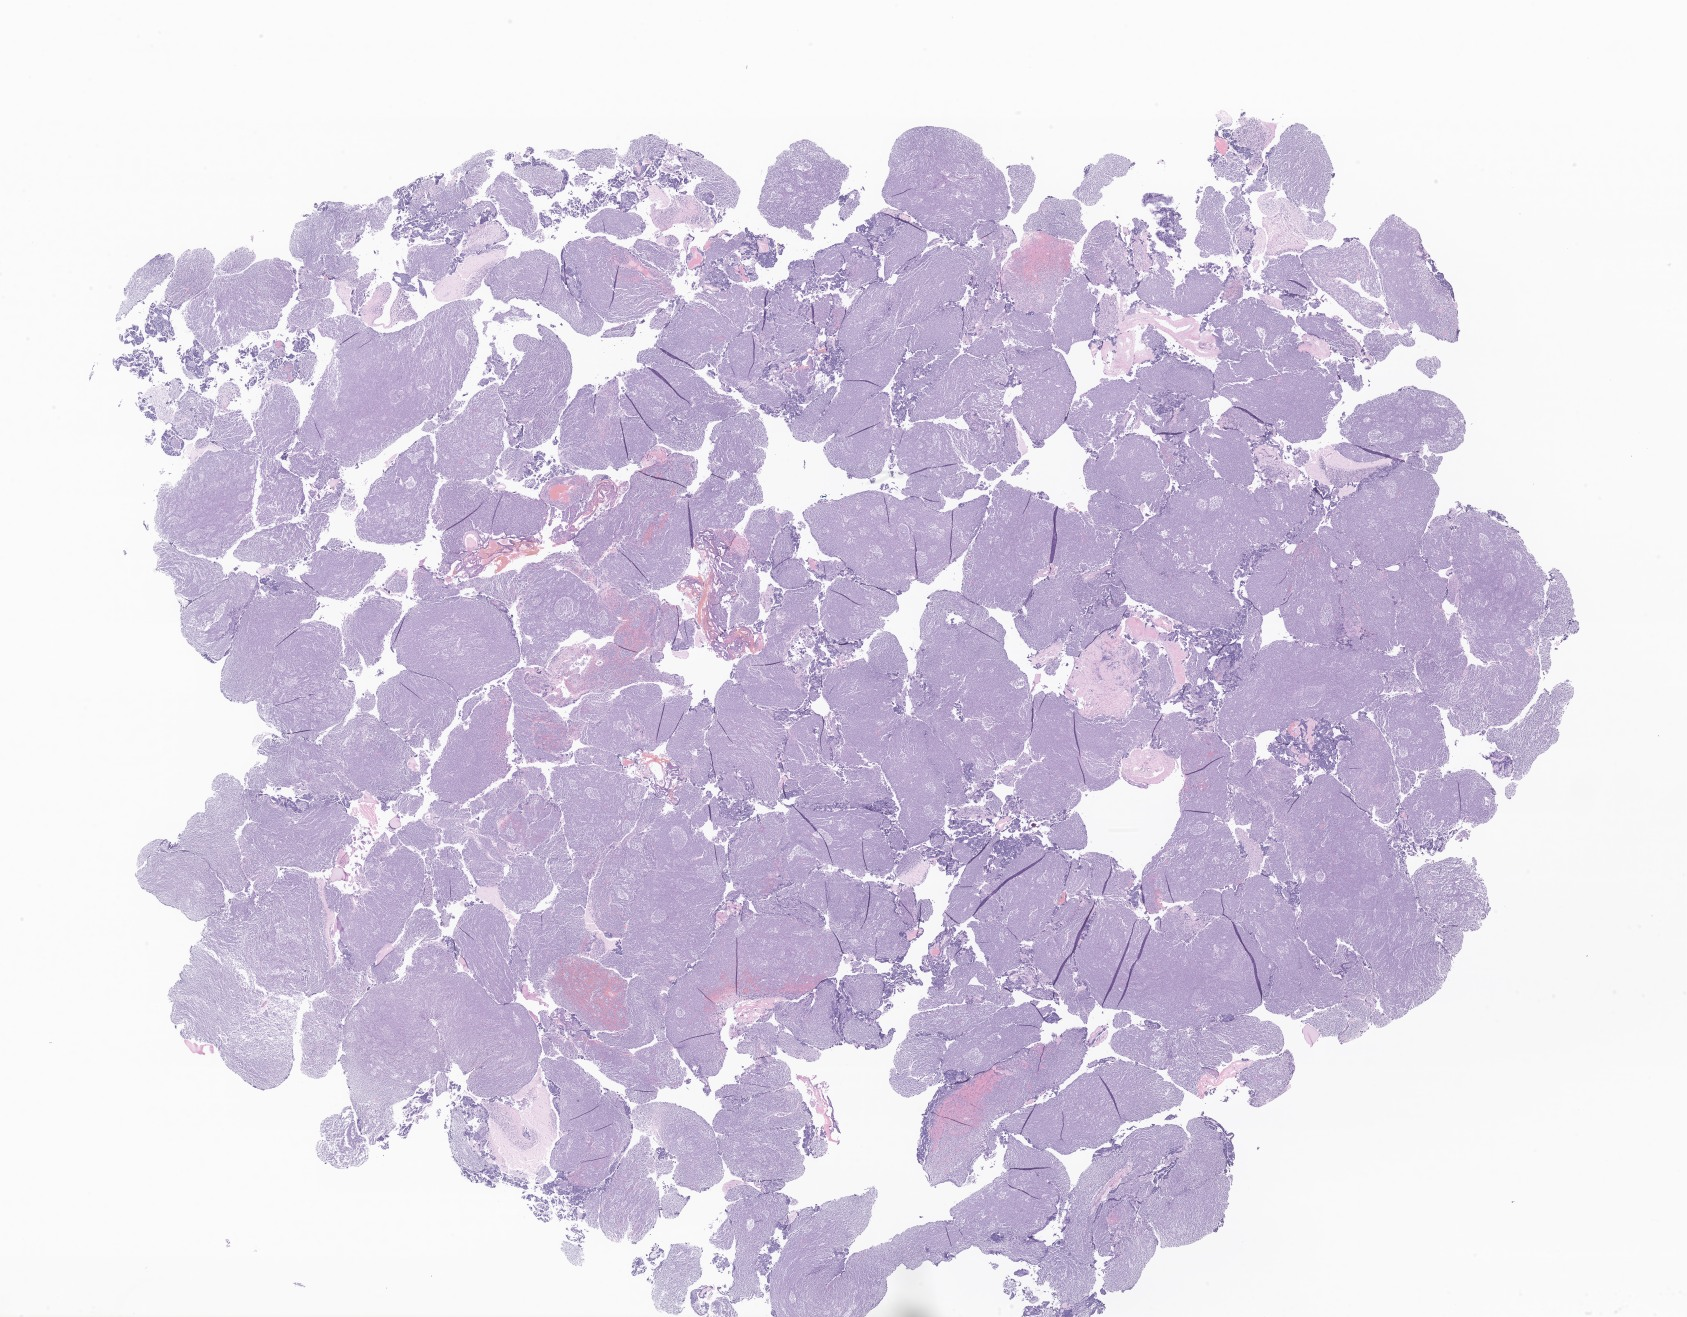
Whole-slide image, H&E stain of tumor tissue from the cerebellum, whole scanned area (about 28.5 x 22.2 mm) shown as a low-resolution overview. FFPE section. Patient female; age 170 months (14 years 2 months).
Recorded diagnosis: Medulloblastoma, NOS.